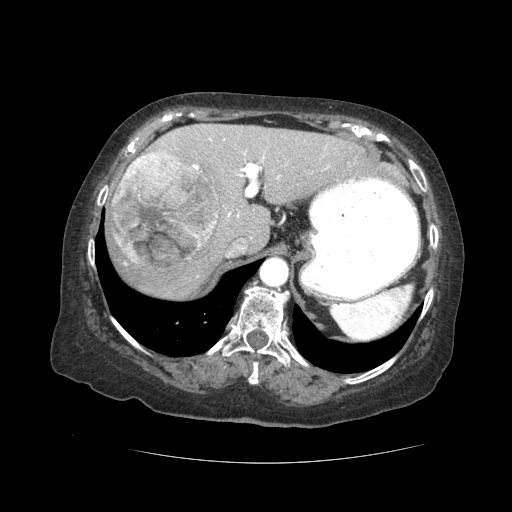
Contrast-enhanced abdominal CT (liver protocol), one axial slice; slice 31 of 59 in the series (ordered by position); 120 kVp; soft-tissue window (W 400 / L 40 HU); 2.5 mm slice thickness; 512 × 512 image matrix. From the clinical record (not read from this slice): diagnosis: hepatocellular carcinoma (patient treated with transarterial chemoembolisation; whether this scan precedes or follows treatment is not stated here); TNM stage (as recorded): Stage-I; Child-Pugh class: A; tumour nodularity: uninodular.
Structures marked on this image (semi-automatic segmentation, software-assisted and operator-edited):
- abdominal aorta: bounding box (x1, y1, x2, y2) in pixels: (260, 259, 287, 288)
- liver parenchyma outside the tumour (the mass and vessels are separate outlines, so this box may not span the whole liver): (108, 124, 366, 298)
- mass: (113, 150, 218, 271)
- liver vessels: (172, 135, 328, 217)